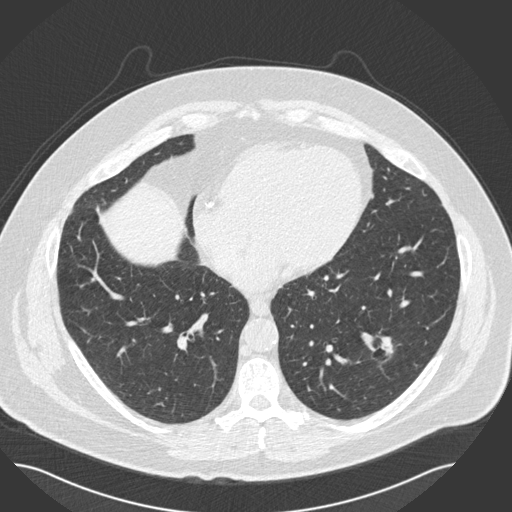
Chest CT (low-dose screening protocol), one axial image. Second annual screen. Lung window (W 1500 / L -600 HU). 2 mm slice thickness. Slice 89 of 162 in the series. 512 × 512 image matrix. Male participant, aged 57 years at enrolment. Current smoker at enrolment.
Lesion marked by an expert reader, bounding box <347,325,414,376> (left, top, right, bottom; pixels). Screening reader's record for this exam (one nodule recorded; not confirmed to be the boxed lesion): non-calcified nodule or mass ≥4 mm, left lower lobe, 19 × 15 mm, pre-existing on the prior screen: yes; interval growth: no. Participant outcome: lung cancer diagnosed 434 days after this screen — squamous cell carcinoma, NOS, left lower lobe, moderately differentiated (G2), stage IA (AJCC 6th edition), 22 mm at pathology.